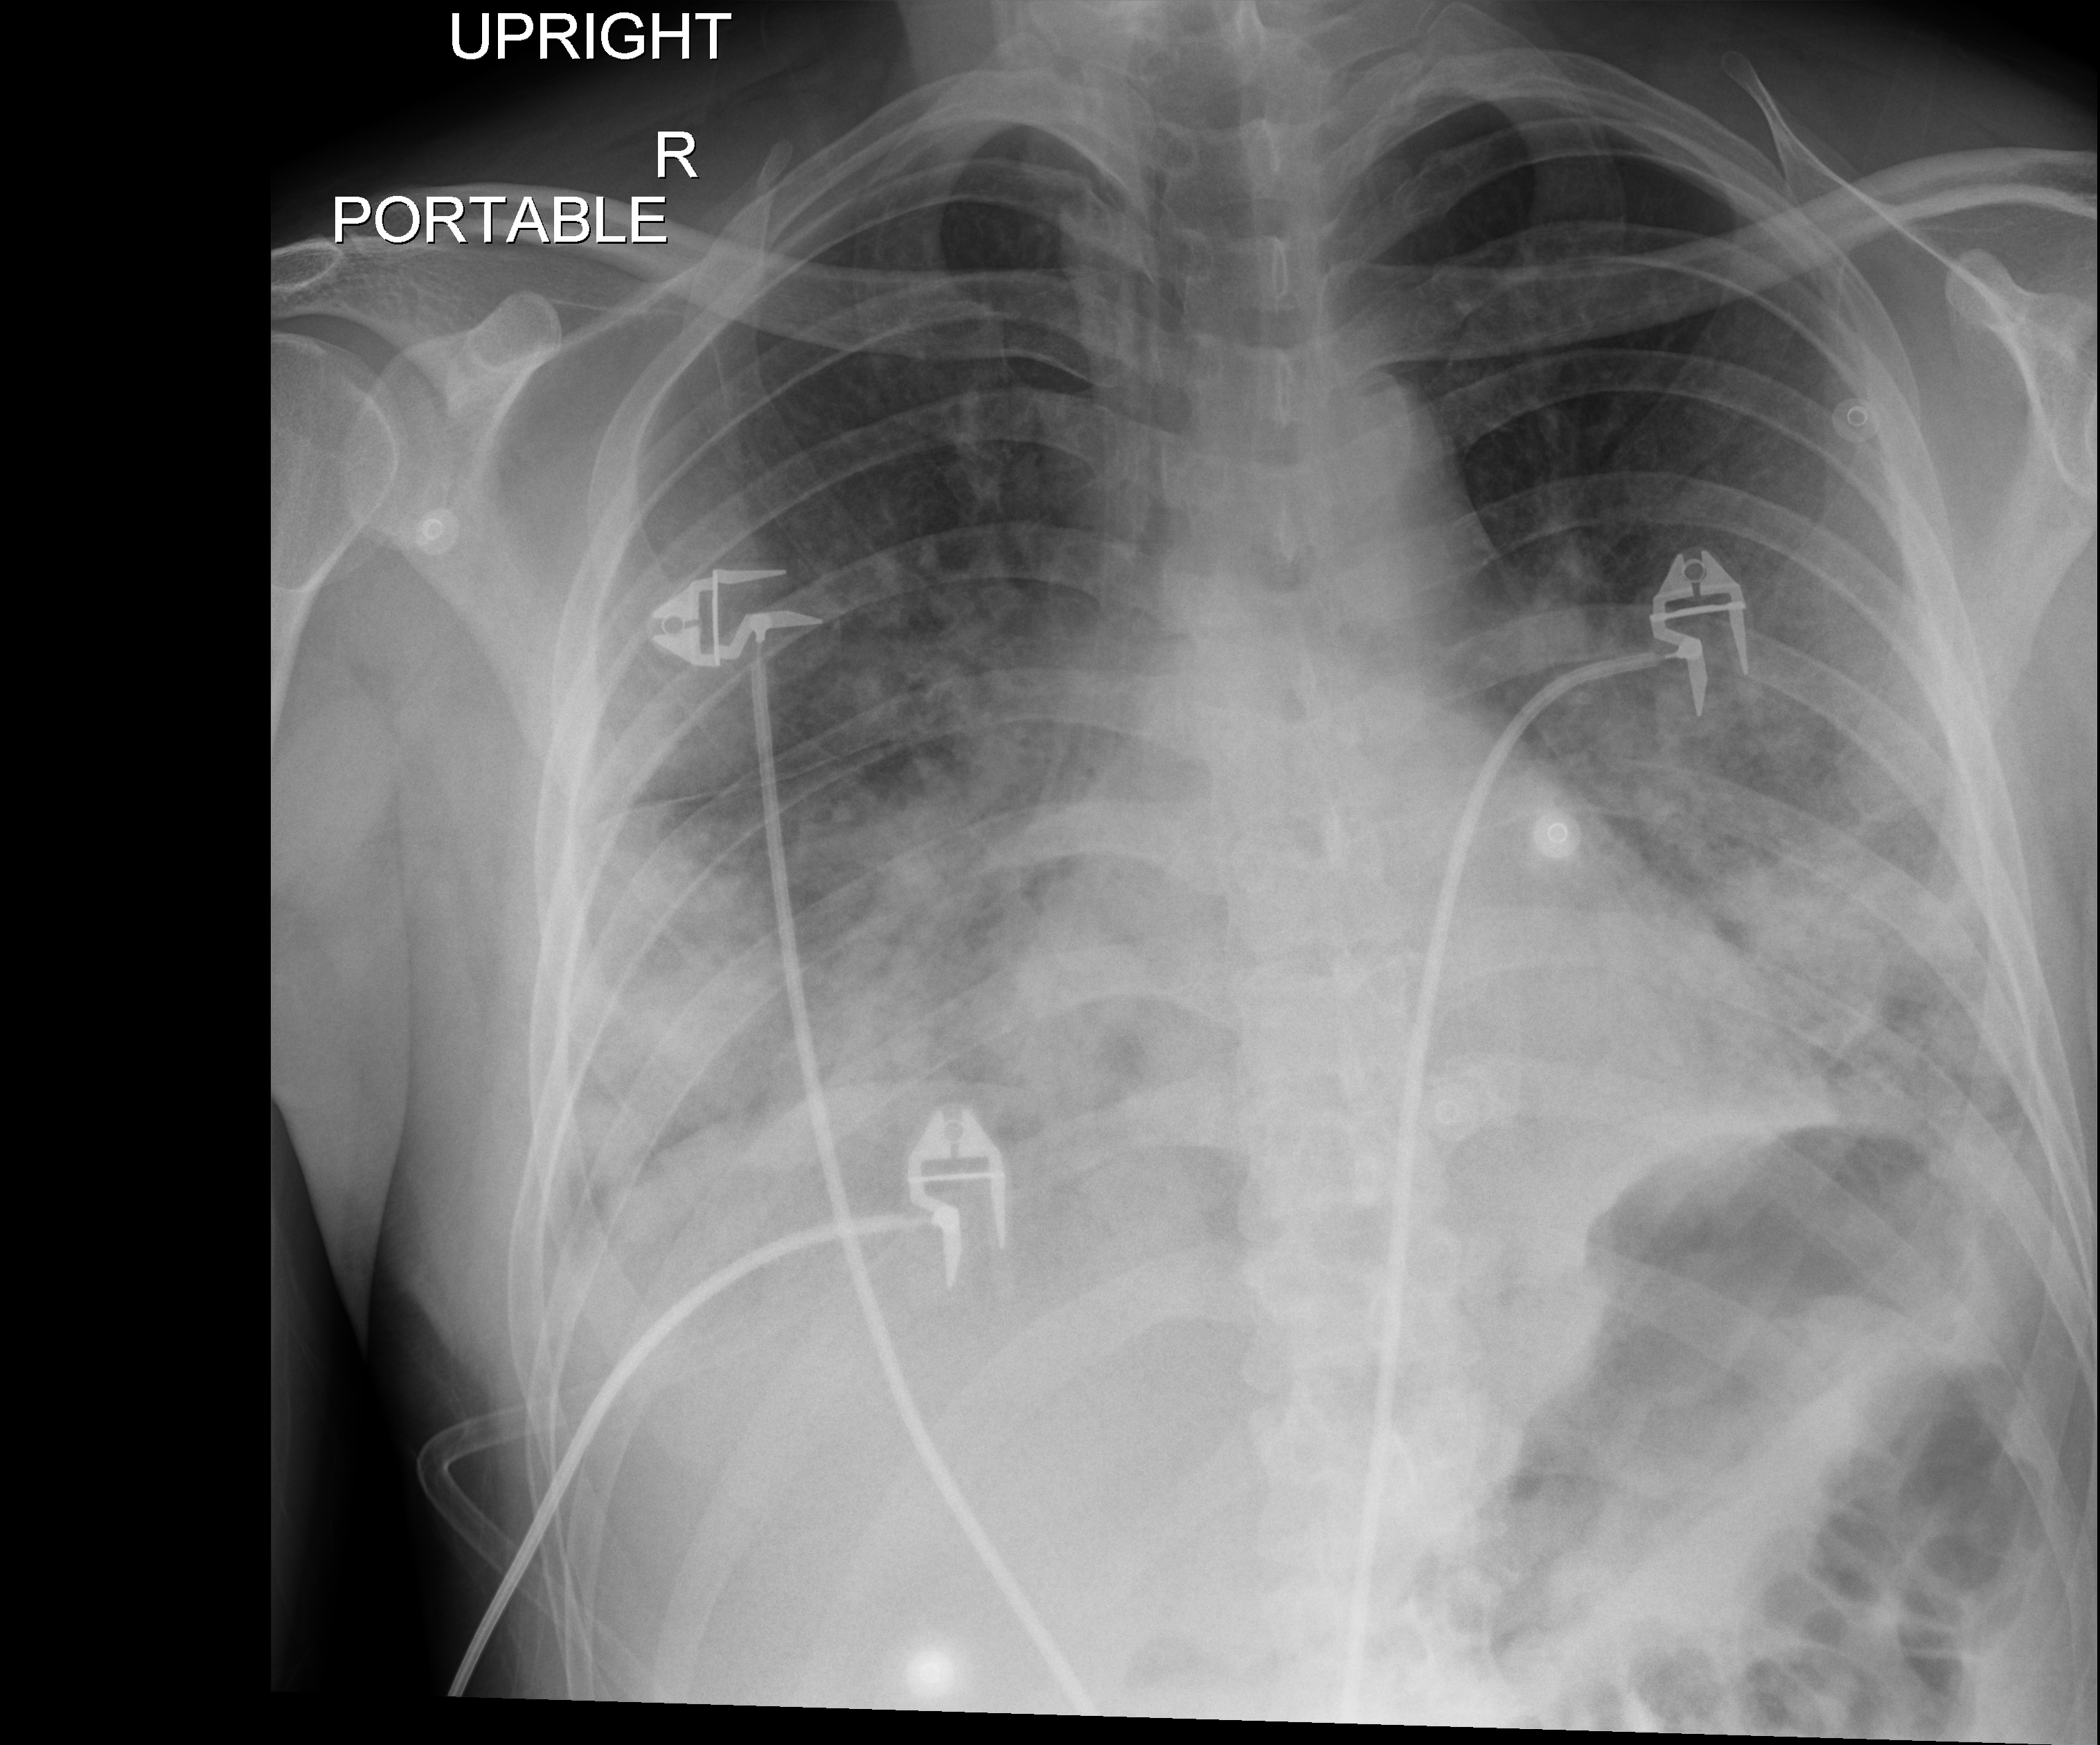
Bedside chest radiograph (digital radiography); anteroposterior (AP) projection. Patient hospitalised with COVID-19; male, aged 18–59 years.
Admission-level facts for this patient (not findings on this image; timing relative to this image not recorded):
- hypertension (admission record): no
- admitted to intensive care during this hospital stay: no